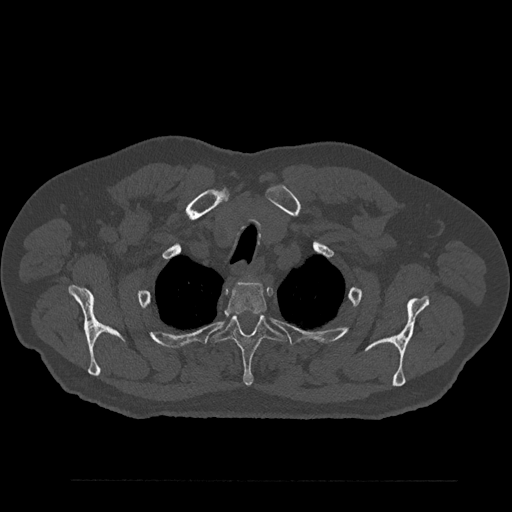
CT including the spine, one axial slice. Position 696 of 797 along the scan axis. Reconstruction kernel Br40s/3. 120 kVp. Bone window (W 1800 / L 400 HU). 512 × 512 image matrix, field of view 430 × 430 mm. Male patient, age 61 years. Case-level facts recorded for this patient, not image findings: primary cancer: prostate.
Outlined on this slice (semi-automatically segmented with operator editing):
- T2 vertebra: bounding box <225,281,267,315> (left, top, right, bottom; pixels)
- T3 vertebra: <213,314,284,386>